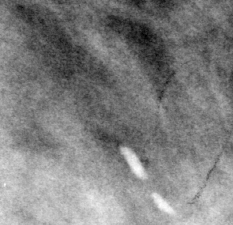
Crop from a digitized film mammogram around one marked abnormality; left breast; MLO view; BI-RADS breast density category 3 (scale 1–4).
- Calcifications, morphology vascular / coarse; BI-RADS assessment category 2; subtlety rating 3 on a 1 (subtle) to 5 (obvious) scale; benign without callback (not worked up further).